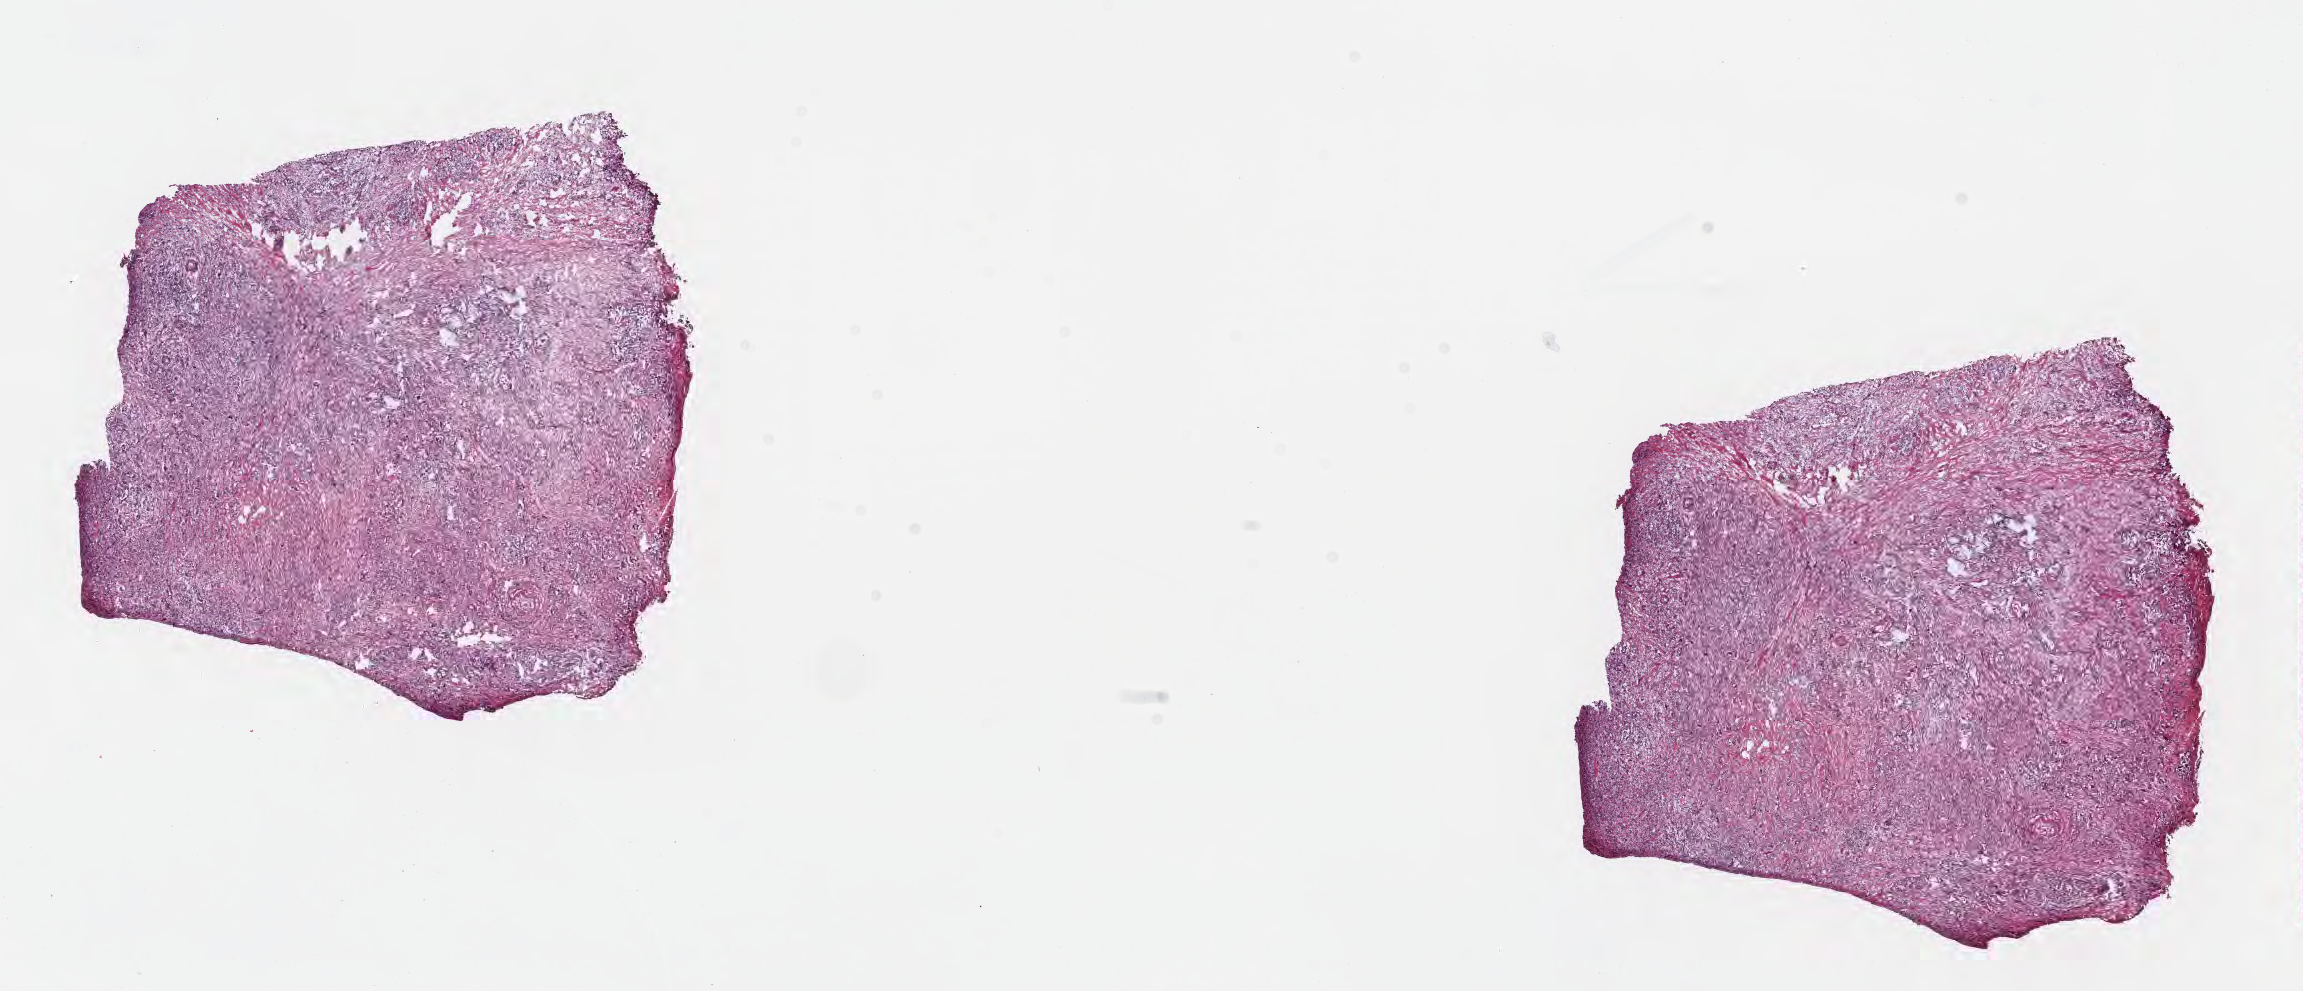
Haematoxylin and eosin whole-slide image, shown as a low-resolution overview of the whole scanned area (about 18.6 x 8.0 mm); frozen section; primary tumor; site: head of pancreas. Female, age 60 years at initial diagnosis. Tumor grade: G3 (poorly differentiated). Pathologist review of this section (percent, as recorded): tumor cells 46%, tumor nuclei 50%, stromal cells 53%, necrosis 1%, normal cells 0%. Infiltration values recorded for this section: lymphocyte infiltration 45%, monocyte infiltration 2%, neutrophil infiltration 0%.
Histologic diagnosis: Infiltrating duct carcinoma, NOS. AJCC pathologic stage: Stage III.